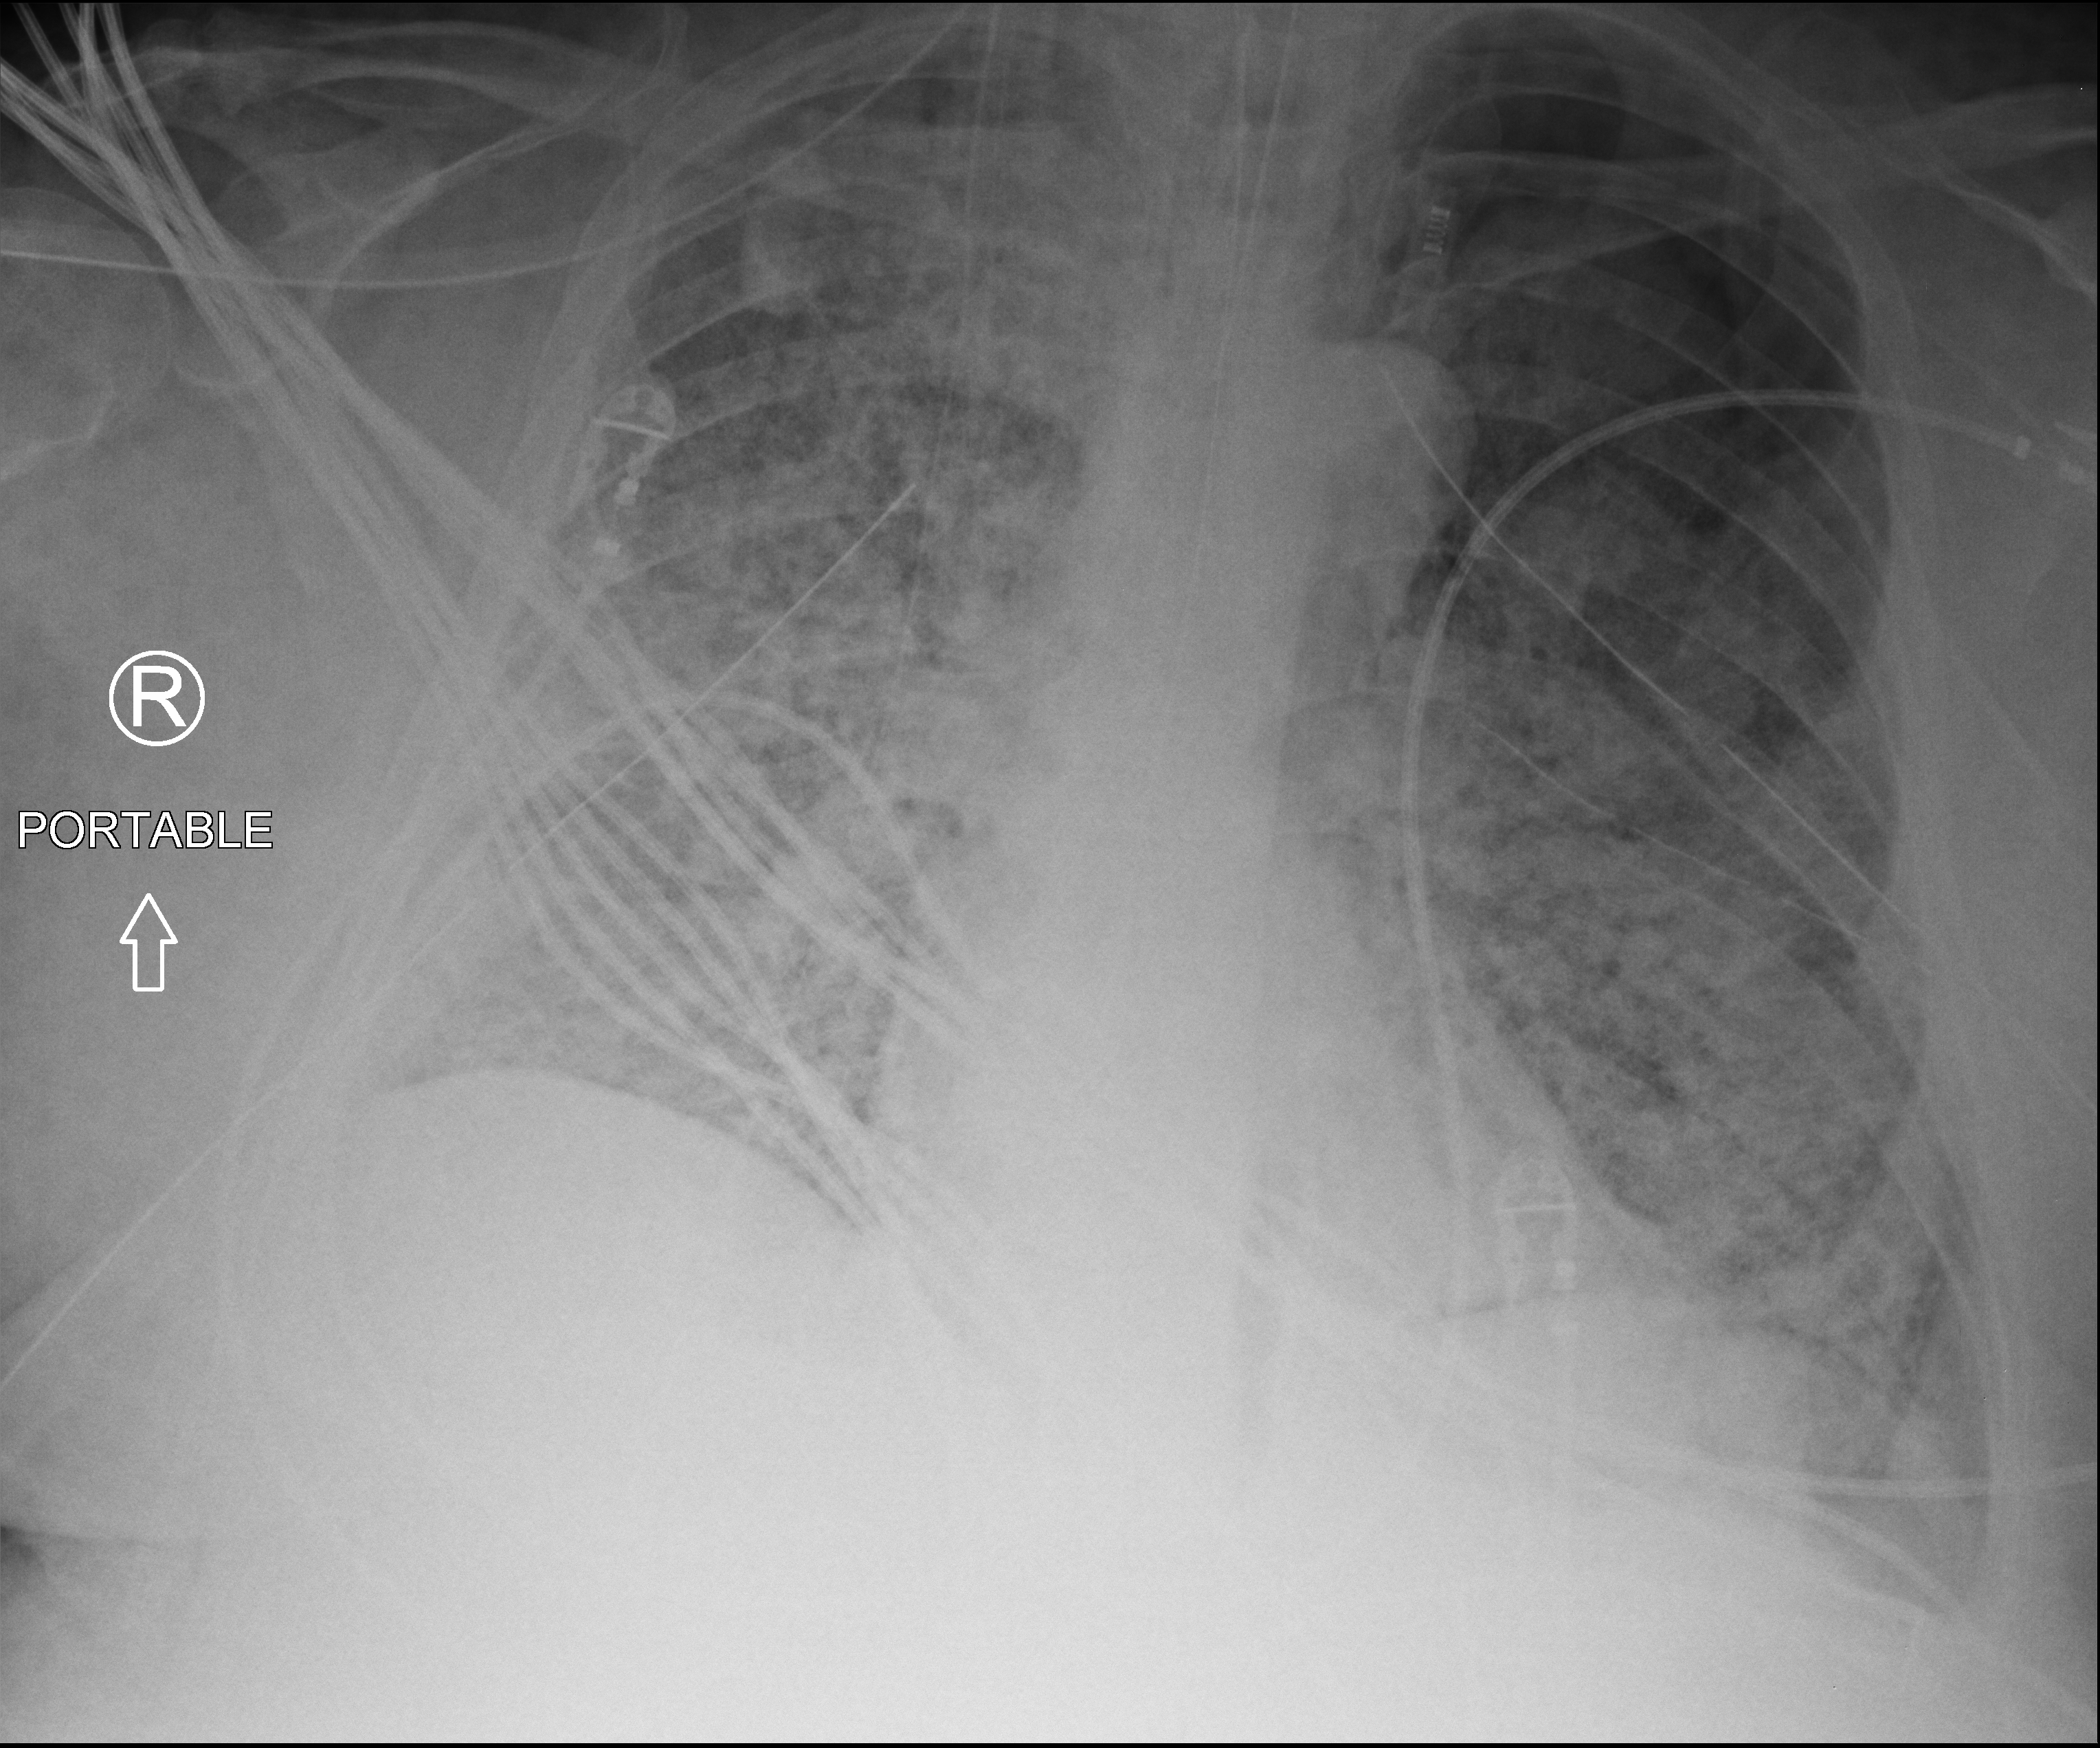
Bedside chest radiograph (computed radiography). Patient hospitalised with COVID-19, aged 18–59 years.
From the hospital-stay record, not from the radiograph (when in the stay this image was taken is not recorded): mechanically ventilated during this hospital stay: yes; length of hospital stay: 28 days.